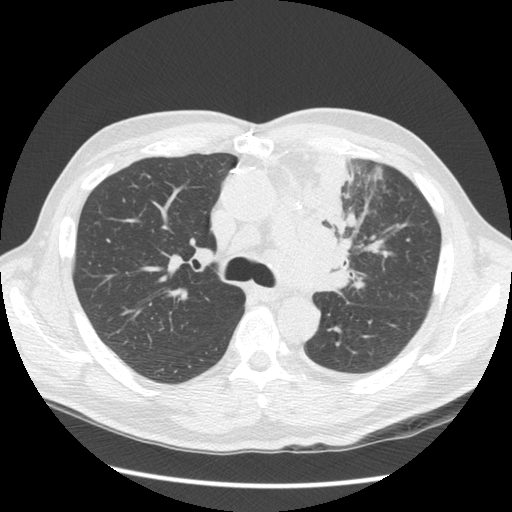
Low-dose screening chest CT, one axial slice; position 92 of 136 along the scan axis; reconstruction kernel STANDARD; 120 kVp; lung window (W 1500 / L -600 HU); 512 × 512 image matrix, field of view 360 × 360 mm.
Outlined on this slice (expert manual segmentation):
- lesion 1 (tumor, upper lobe of left lung): bounding box [x1, y1, x2, y2] px = [300, 152, 352, 292]